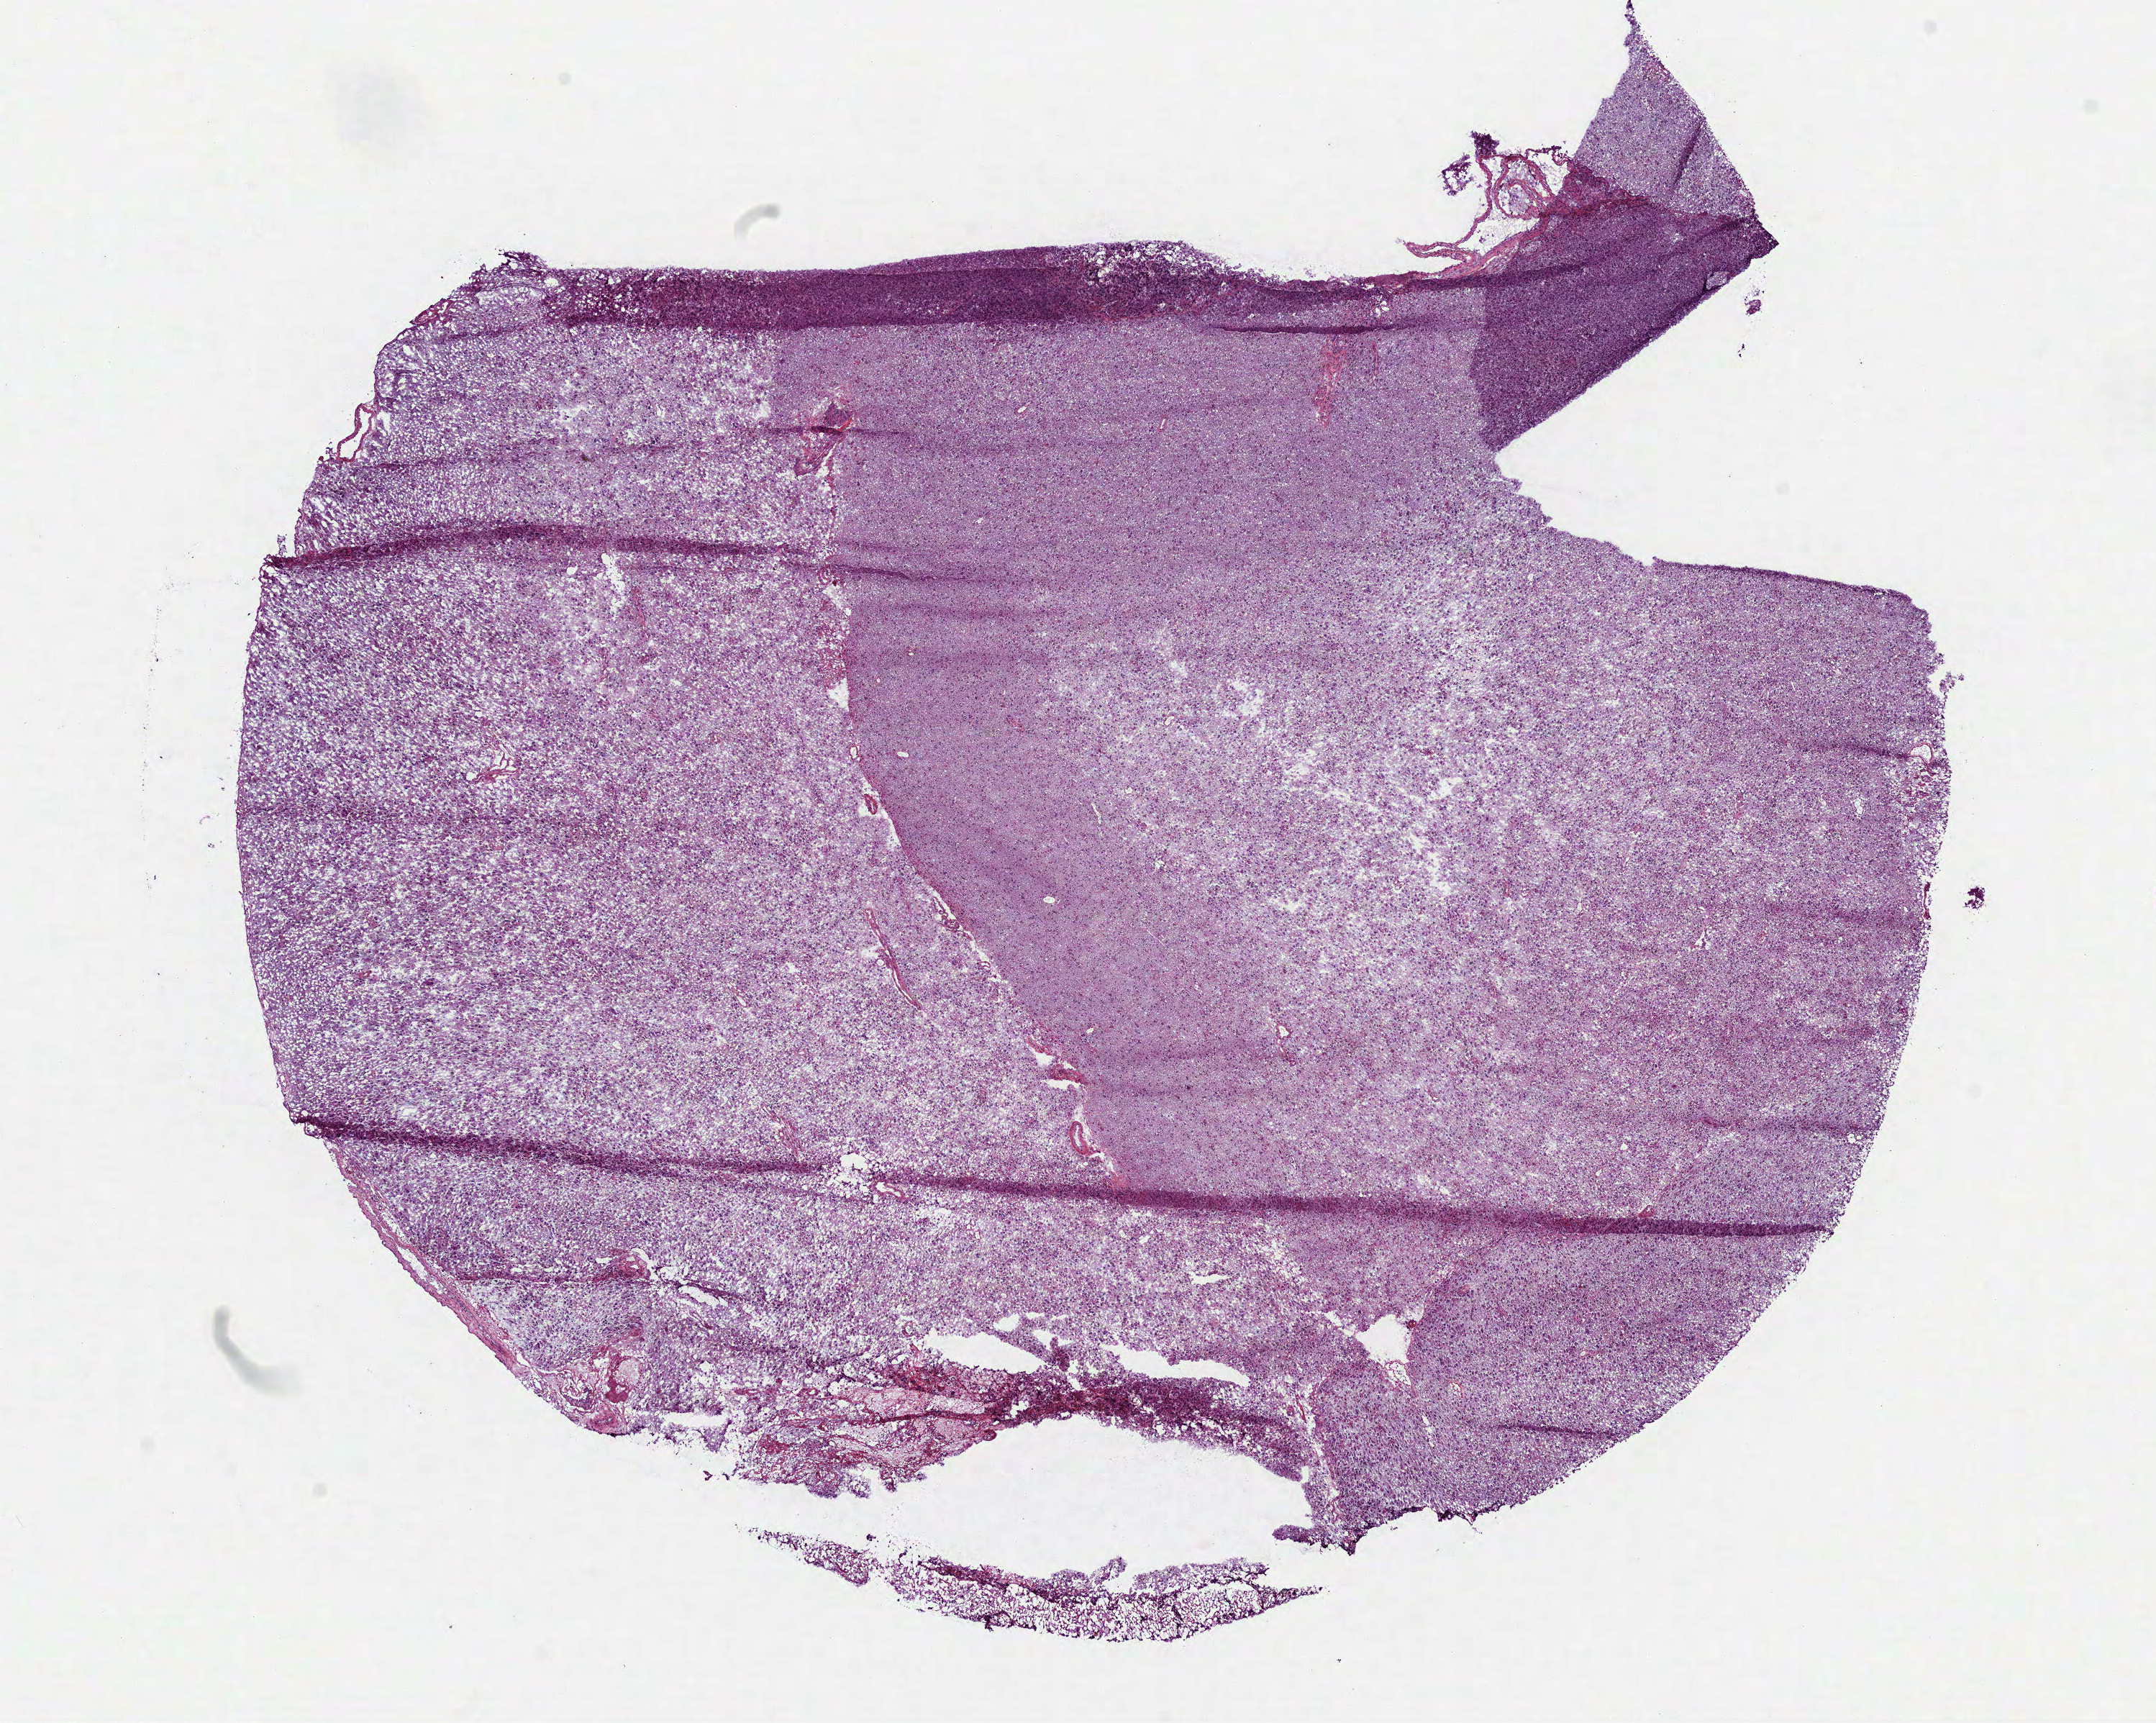
Digitized Hematoxylin and eosin (H&E) stained tissue section (whole slide), a low-resolution overview of the entire scanned area, about 12.1 x 9.7 mm (slide scanned at 40x). Frozen section from the bottom of the tissue portion. Brain, primary tumour sample. Male, age 39 years at initial diagnosis. Composition of this section per pathologist review: tumour cells 100%, tumour nuclei 65%, normal cells 0%, stromal cells 0%, necrosis 0%.
• pathologic diagnosis: Mixed glioma (cerebrum)
• laterality: right